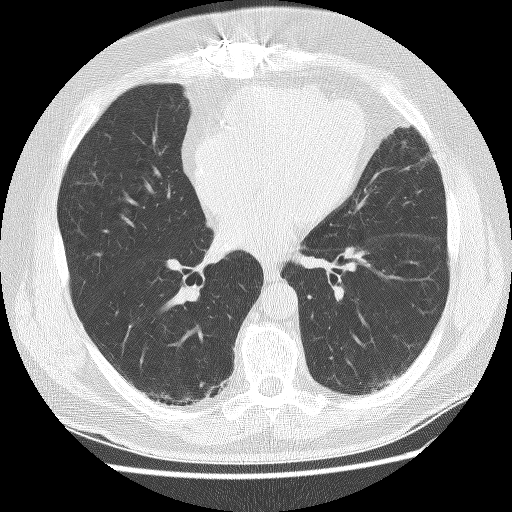
Chest CT (low-dose screening protocol), one axial image; first (baseline) screen; lung window (W 1500 / L -600 HU); 2.5 mm slice thickness; lung (sharp) reconstruction kernel (BONE); 120 kVp; slice 129 of 236 in the series; 512 × 512 image matrix, field of view 340 × 340 mm. Male, age 65 years at enrolment. Former smoker at enrolment.
Expert reader's lesion annotation, bounding box [x1, y1, x2, y2] px = [355, 371, 398, 408]. No non-calcified nodule or mass ≥4 mm was recorded by the screening reader at this exam. Official screen result: negative screen, minor abnormalities not suspicious for lung cancer. Later outcome: lung cancer diagnosed 523 days after this screen (after the second annual screen) — squamous cell carcinoma, NOS, left lower lobe, moderately differentiated (G2), stage IA (AJCC 6th edition), 20 mm at pathology.